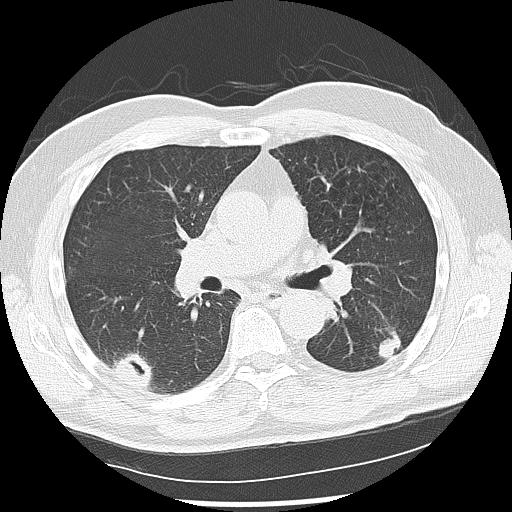
Low-dose screening chest CT, one axial slice. Slice 74 of 142 in the series (ordered by position). Reconstruction kernel LUNG. 120 kVp. Lung window (W 1500 / L -600 HU). 512 × 512 image matrix.
Structures marked on this image (expert manual segmentation):
- lesion 1 (nodule, lower lobe of left lung): bounding box <378,333,401,361> (left, top, right, bottom; pixels)
- lesion 2 (nodule, lower lobe of right lung): <113,352,153,390>